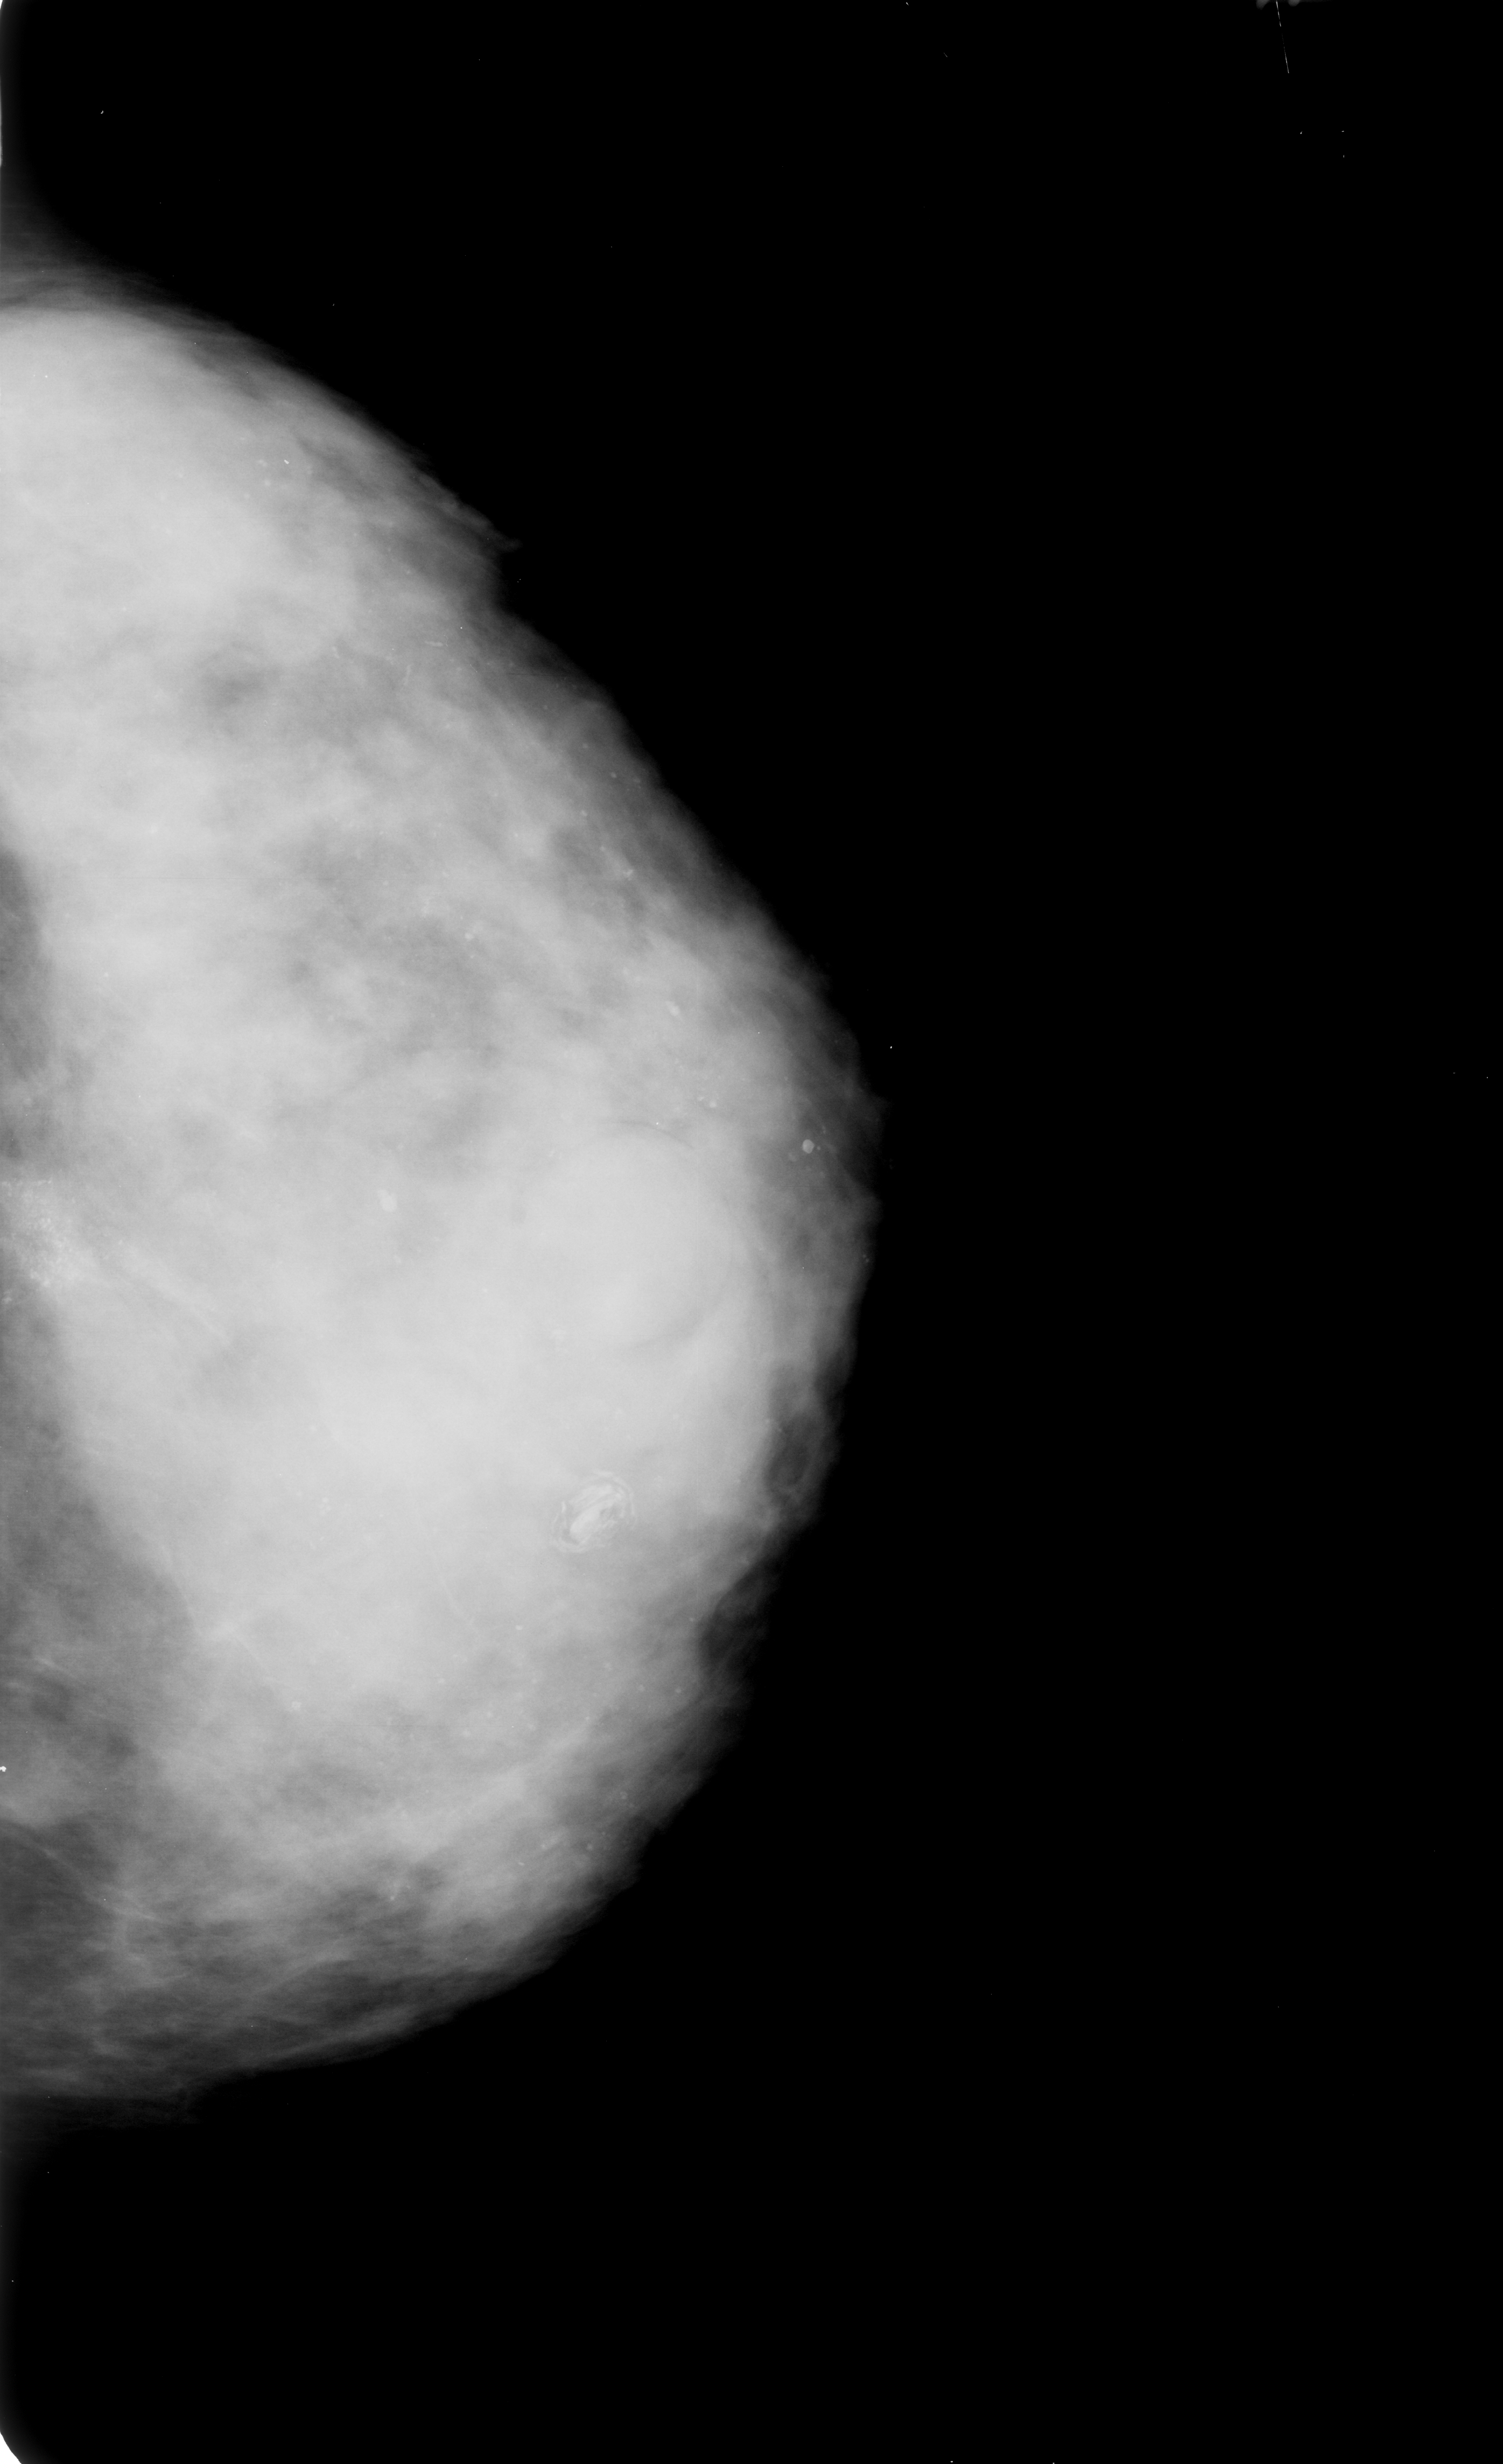
Scanned film-screen mammogram; left breast; craniocaudal (CC) view; 1503 × 2464 image matrix.
Marked abnormalities (boxes around the expert regions of interest):
- mass, shape round, margins circumscribed; BI-RADS assessment category 3; subtlety rating 3 on a 1 (subtle) to 5 (obvious) scale; pathology result (as recorded, not read from the image): benign: bounding box <546,1125,756,1332> (left, top, right, bottom; pixels)